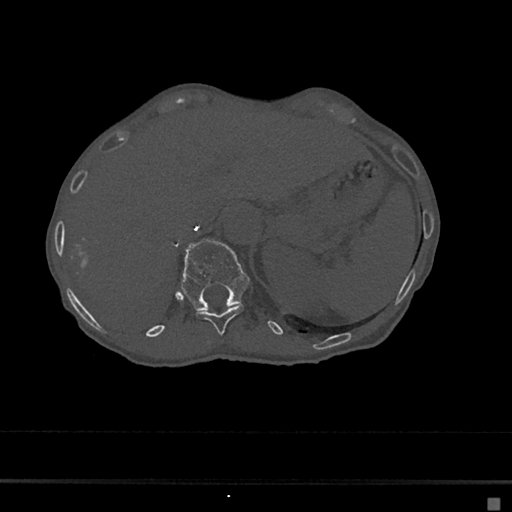
CT including the spine, one axial slice; slice 146 of 797 in the series (ordered by position); bone window (W 1800 / L 400 HU); 512 × 512 image matrix, field of view 360 × 360 mm. Female patient, age 68 years. Case-level facts recorded for this patient, not image findings: primary cancer: renal.
Outlined on this slice (semi-automatically segmented with operator editing):
- T11 vertebra: bounding box <195,304,244,335> (left, top, right, bottom; pixels)
- T12 vertebra: <181,239,250,311>